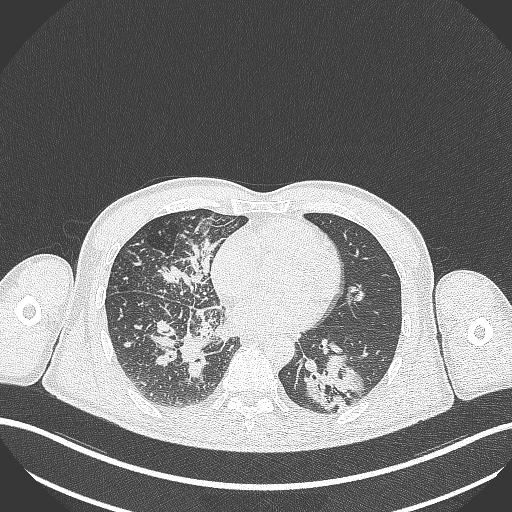
Chest CT, one axial slice. Slice 127 of 348 in the series (ordered by position). Reconstruction kernel B70f. Lung window (W 1500 / L -600 HU). 512 × 512 image matrix, field of view 400 × 400 mm. Male patient, age 49 years. Case-level facts recorded for this patient, not image findings: clinical TNM (as recorded): T2b N1 M0.
Outlined on this slice (rectangle marked by the reading radiologist):
- lung tumour (recorded histology: adenocarcinoma): box from (x=305, y=355) to (x=364, y=414) px